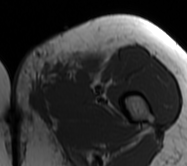
MRI of an extremity soft-tissue mass, one axial slice. MR volume resampled by the dataset authors to the PET/CT grid (not the native acquisition matrix). 187 × 166 image matrix, field of view 183 × 162 mm. Female patient. Case-level facts recorded for this patient, not image findings: histological type: leiomyosarcoma; grade: high; site of the primary tumour: groin.
Annotated regions visible in this slice (expert contour drawn on MRI and transferred to this co-registered scan by the dataset authors):
- gross tumour volume including surrounding oedema: box from (x=13, y=42) to (x=101, y=120) px
- gross tumour volume (mass): (x=50, y=55)–(x=99, y=86)